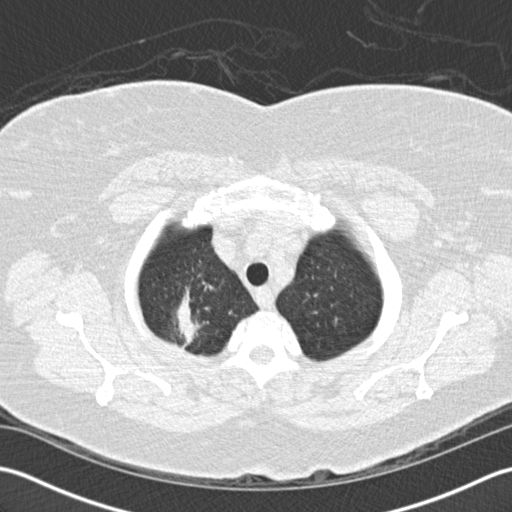
Axial slice from a low-dose chest CT screening exam; baseline screening round; lung window (W 1500 / L -600 HU); standard (soft-tissue) reconstruction kernel (B30f); 120 kVp. Female participant, aged 72 years at enrolment.
- Expert-annotated lung lesion, bounding box <135,277,224,367> (left, top, right, bottom; pixels).
- The screening reader recorded 2 non-calcified nodules or masses ≥4 mm on this exam (right lower lobe, right lower lobe); which of them this box marks is not recorded.
- Official screen result: positive, change unspecified: nodule(s) >= 4 mm or enlarging nodule(s), mass(es), or other non-specific abnormalities suspicious for lung cancer.
- Participant outcome: lung cancer diagnosed 494 days after this screen — bronchiolo-alveolar adenocarcinoma, NOS, right upper lobe, stage IIIB (AJCC 6th edition), 45 mm at pathology.